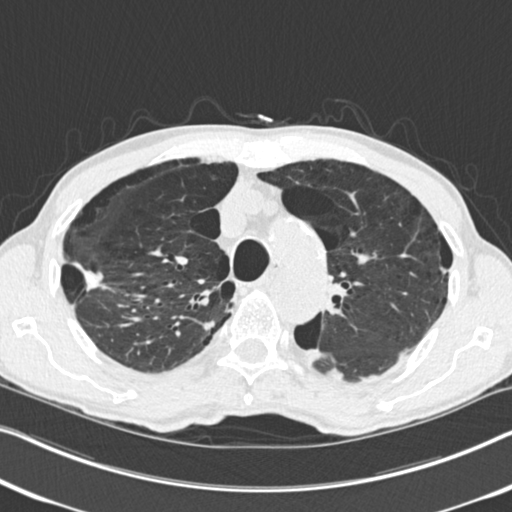
Low-dose screening chest CT, one axial slice; position 185 of 251 along the scan axis; reconstruction kernel B30f; 120 kVp; lung window (W 1500 / L -600 HU); 2 mm slice thickness; 512 × 512 image matrix, field of view 334 × 334 mm.
Structures marked on this image (manually delineated by an expert):
- lesion 1 (tumor, upper lobe of right lung): bounding box [x1, y1, x2, y2] px = [77, 265, 105, 291]